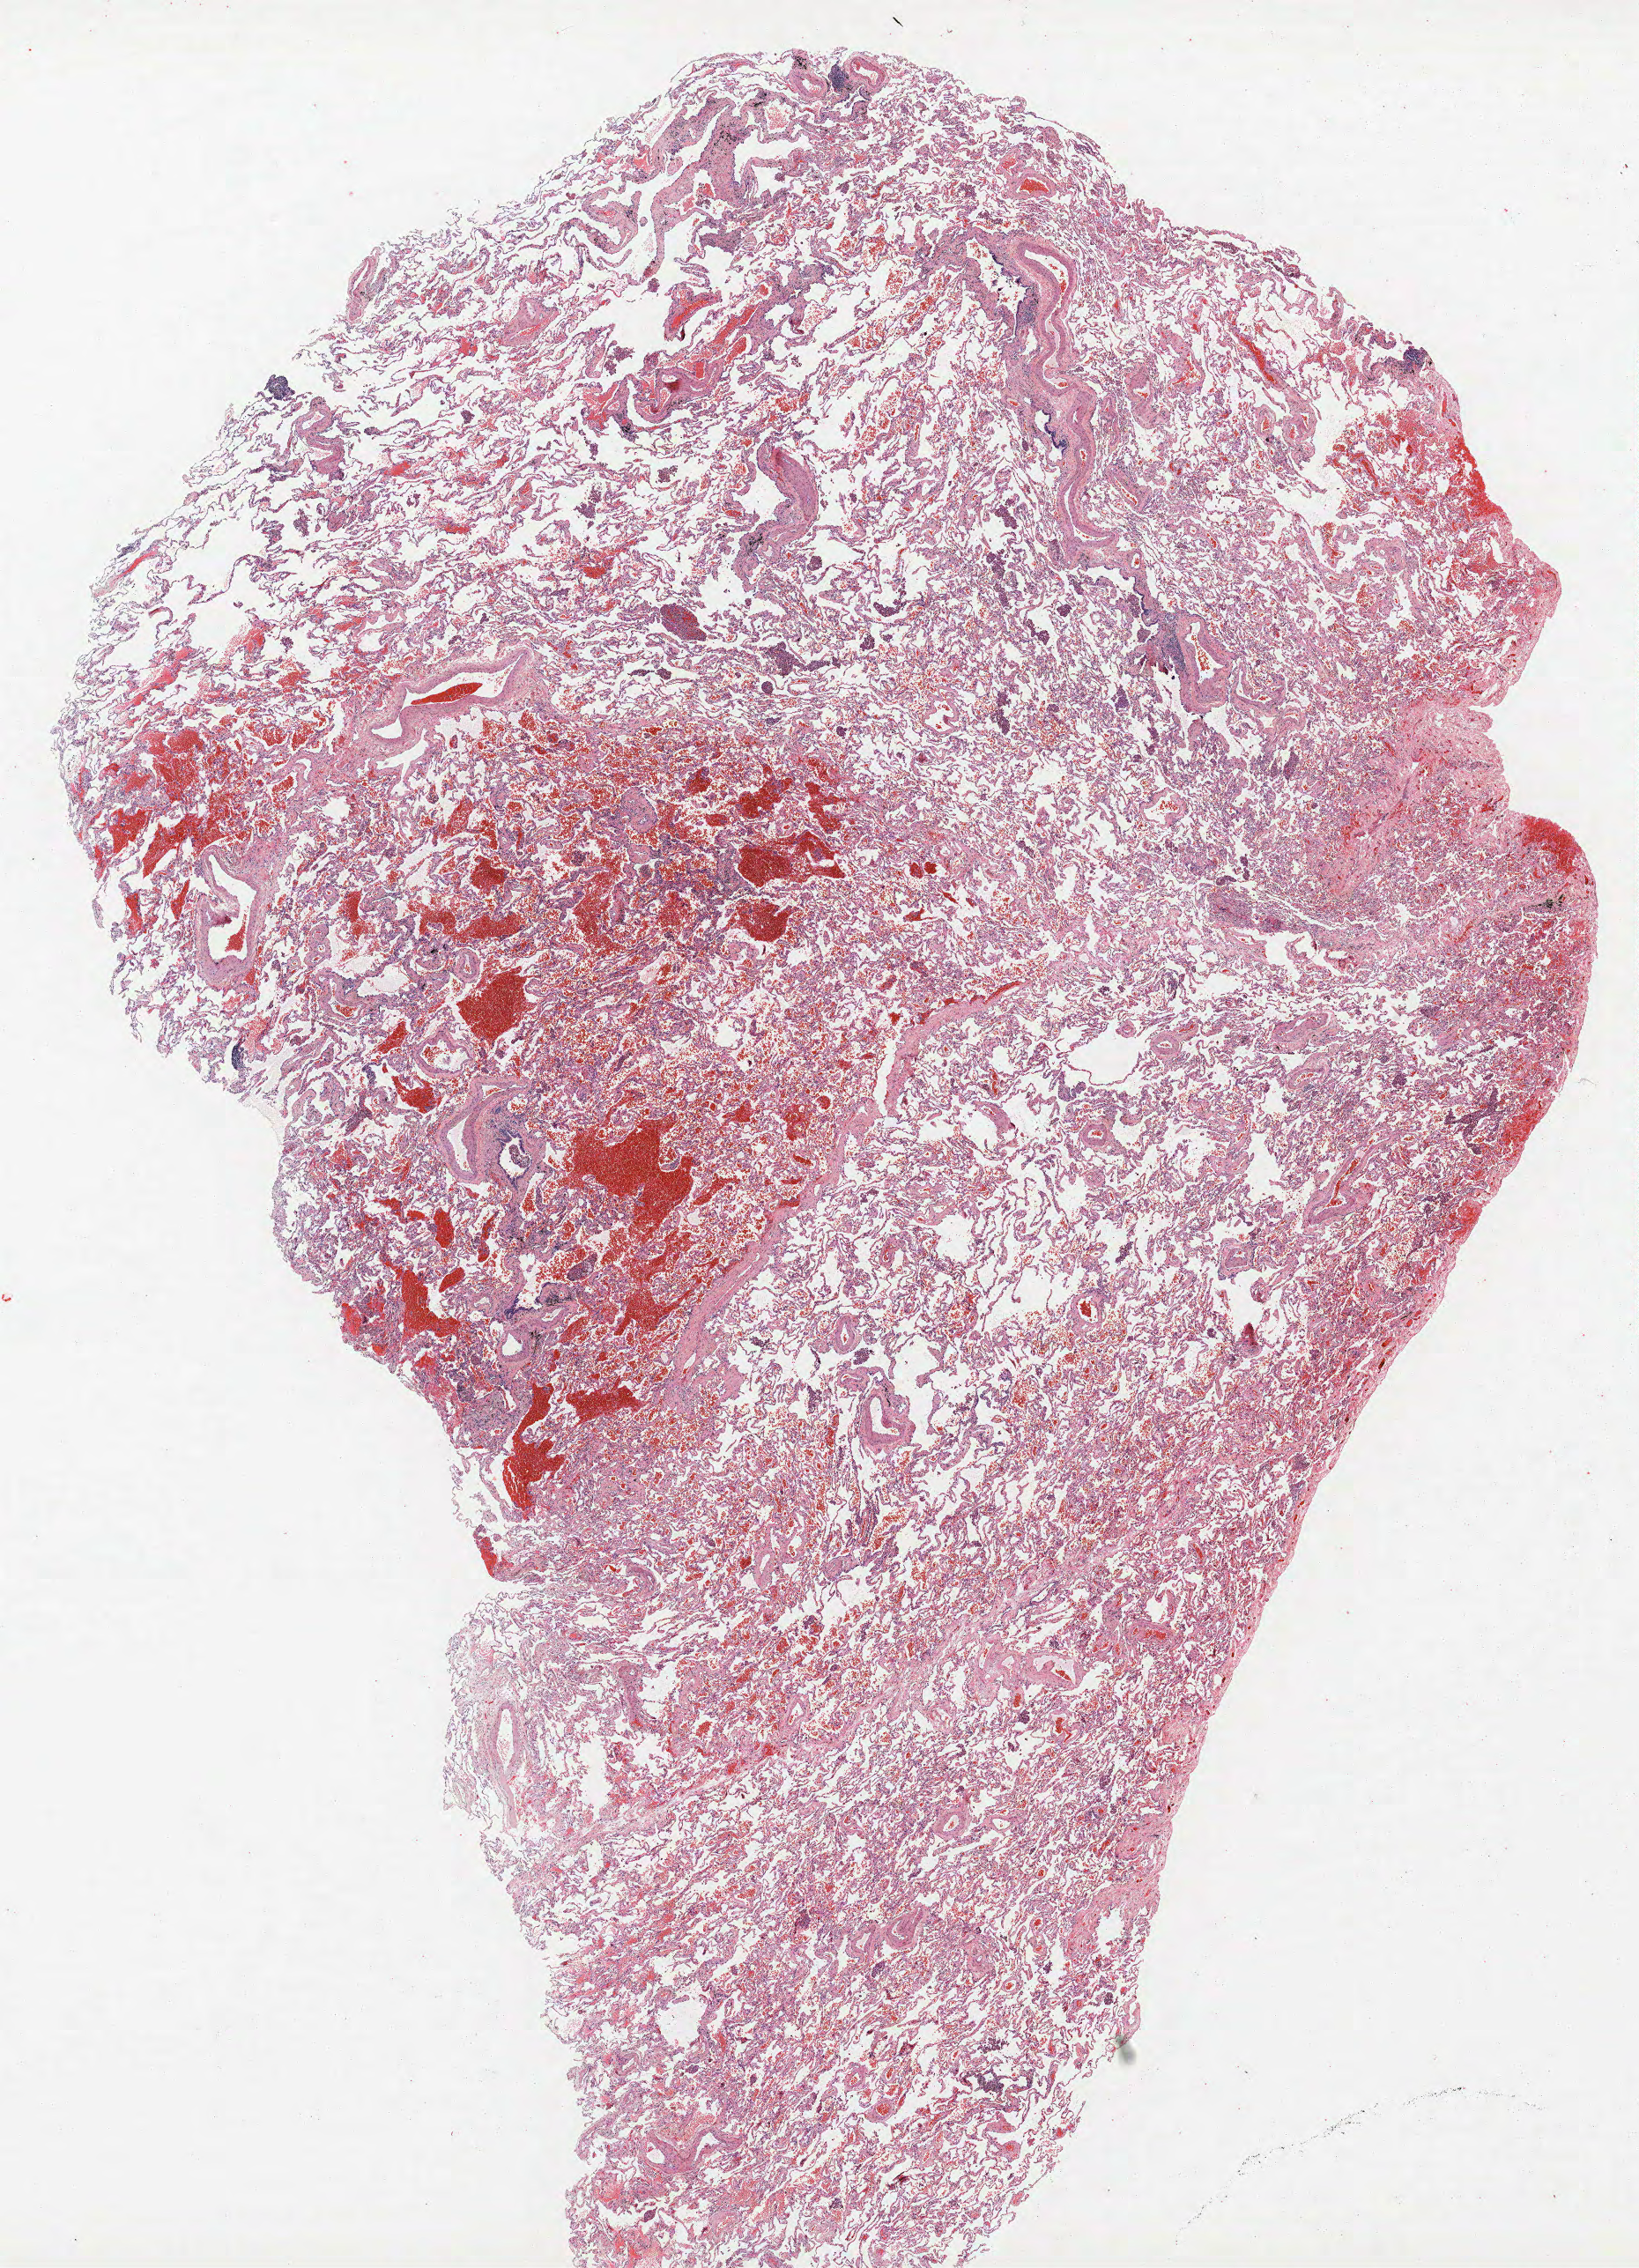
Hematoxylin and eosin (H&E) stained whole-slide image, a low-resolution overview of the entire scanned area, about 14.9 x 20.6 mm. FFPE section. Lung. Female patient, aged 68 at enrolment. Current smoker at enrolment. Grade: undifferentiated (G4).
Stage (AJCC 6th edition): IB. Primary tumour location (clinical record): right upper lobe. Tumour size (pathology): 22 mm. Participant's lung-cancer diagnosis: Large cell neuroendocrine carcinoma.